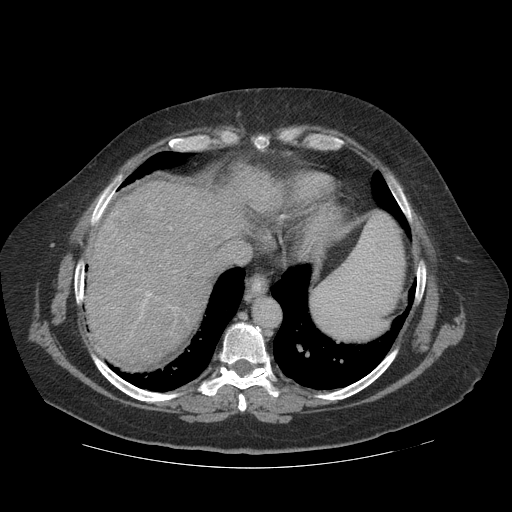
Contrast-enhanced abdominal CT (liver protocol), one axial slice. Slice 99 of 121 in the series (ordered by position). Reconstruction kernel STANDARD. 140 kVp. Soft-tissue window (W 400 / L 40 HU). 2.5 mm slice thickness. 512 × 512 image matrix, field of view 420 × 420 mm. From the clinical record (not read from this slice): diagnosis: hepatocellular carcinoma (patient treated with transarterial chemoembolisation; whether this scan precedes or follows treatment is not stated here); TNM stage (as recorded): Stage-IIIA; Child-Pugh class: A; tumour nodularity: multinodular.
Outlined on this slice (semi-automatically segmented with operator editing):
- abdominal aorta: box from (x=254, y=299) to (x=280, y=328) px
- liver parenchyma outside the tumour (the mass and vessels are separate outlines, so this box may not span the whole liver): (x=86, y=168)–(x=278, y=368)
- mass: (x=110, y=192)–(x=149, y=241)
- liver vessels: (x=137, y=227)–(x=178, y=318)